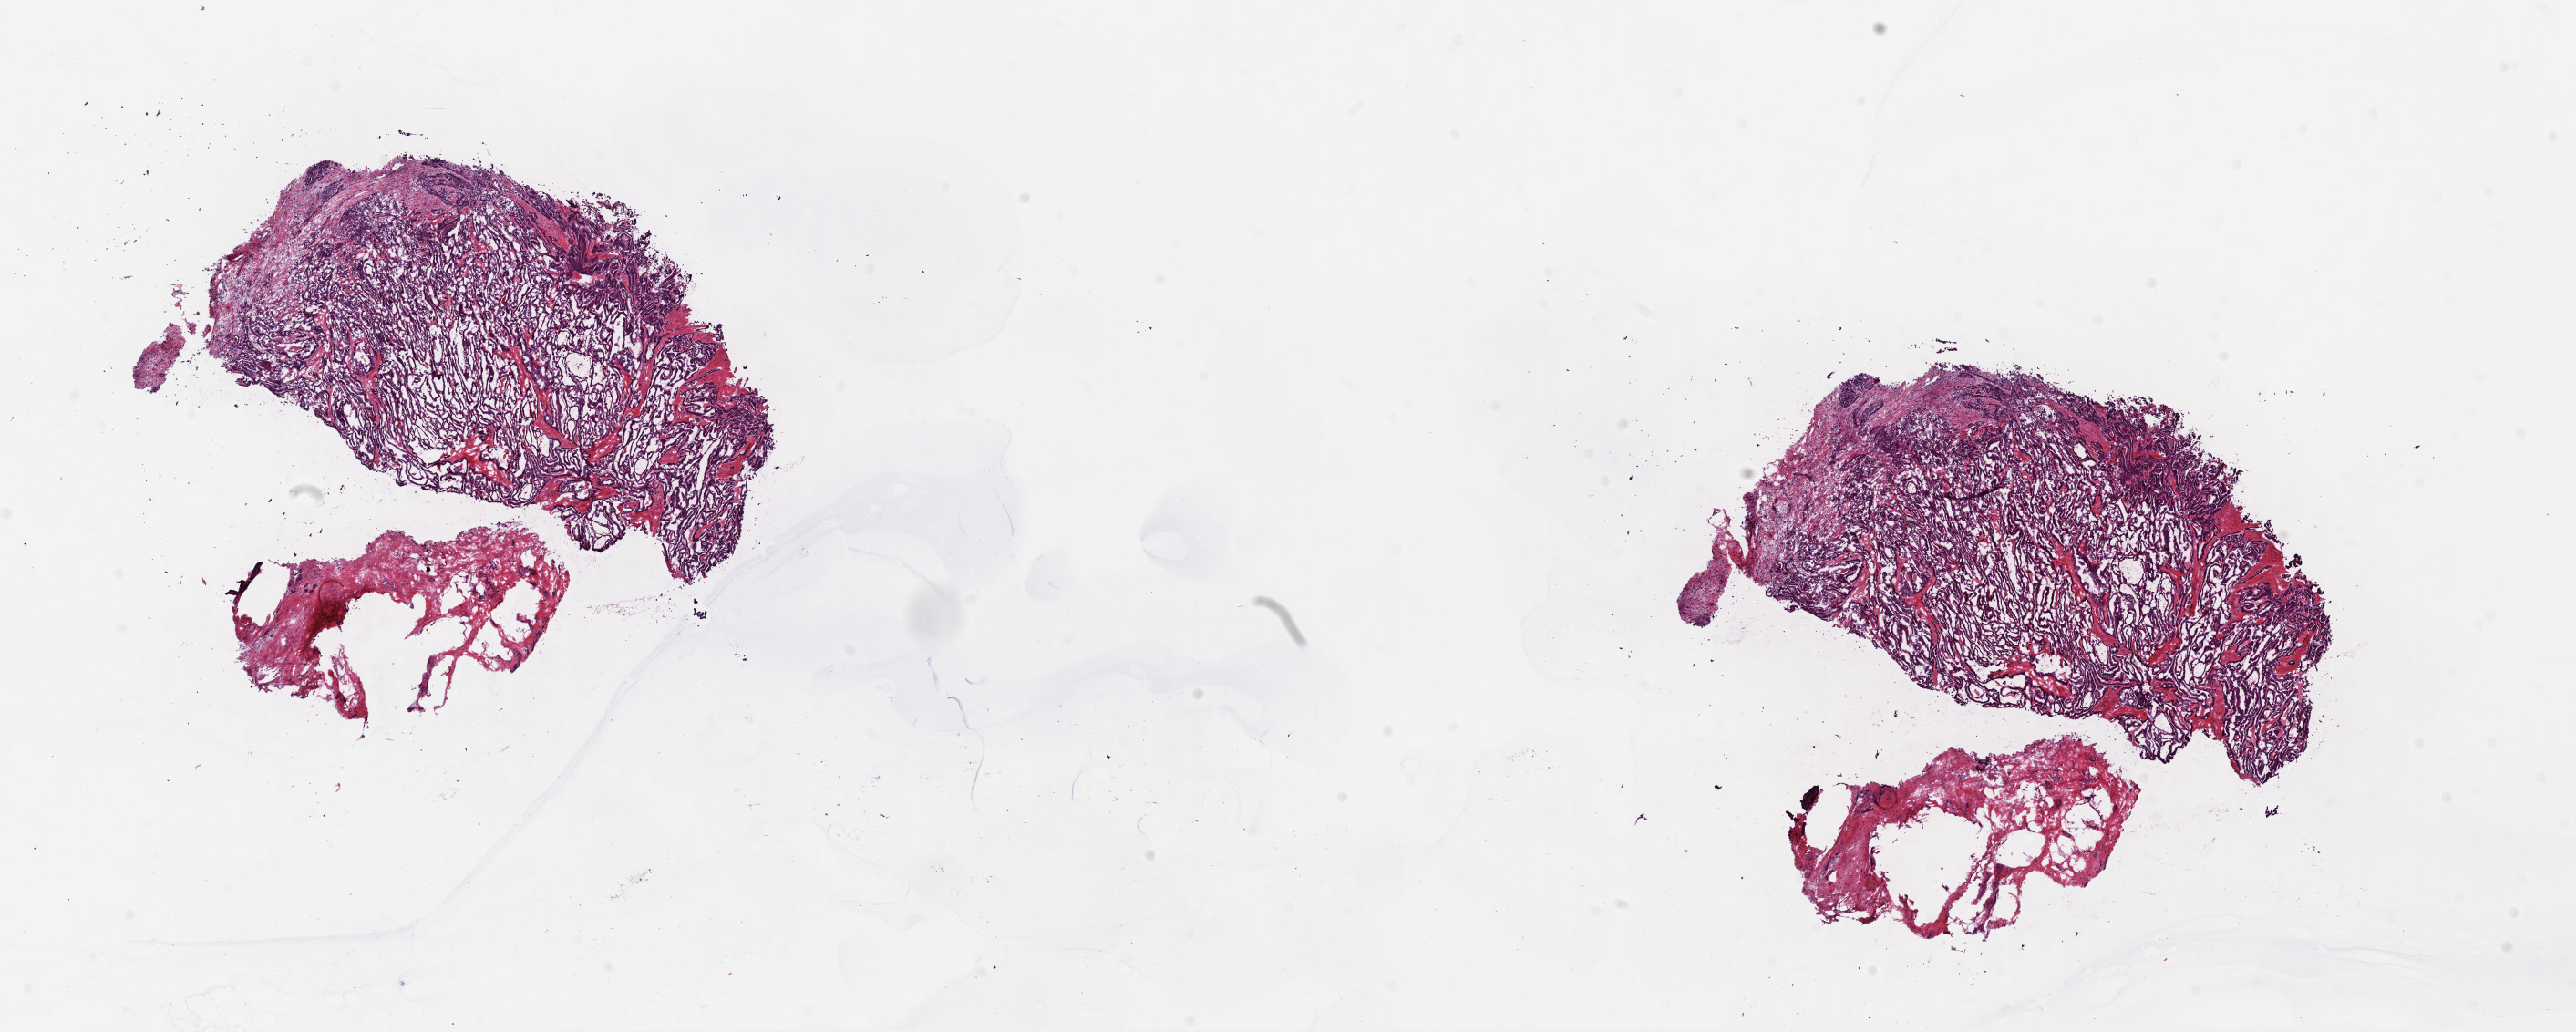
Whole-slide histology image, Hematoxylin and eosin (H&E) stained — a low-resolution overview of the entire scanned area, about 22.3 x 8.9 mm; frozen section; thyroid, primary tumour sample. Female patient; age at initial diagnosis 72 years. Pathologist review of this section (percent, as recorded): tumour cells 85%, tumour nuclei 85%, normal cells 0%, stromal cells 15%, necrosis 0%. Inflammatory infiltration, as recorded: lymphocyte infiltration 0%, monocyte infiltration 0%, neutrophil infiltration 0%.
AJCC pathologic stage: III. Histologic diagnosis: Papillary adenocarcinoma, NOS (thyroid gland). TNM: T3 N1 M0. Lymph nodes positive (case pathology): 10 of 23 examined. Laterality: left.